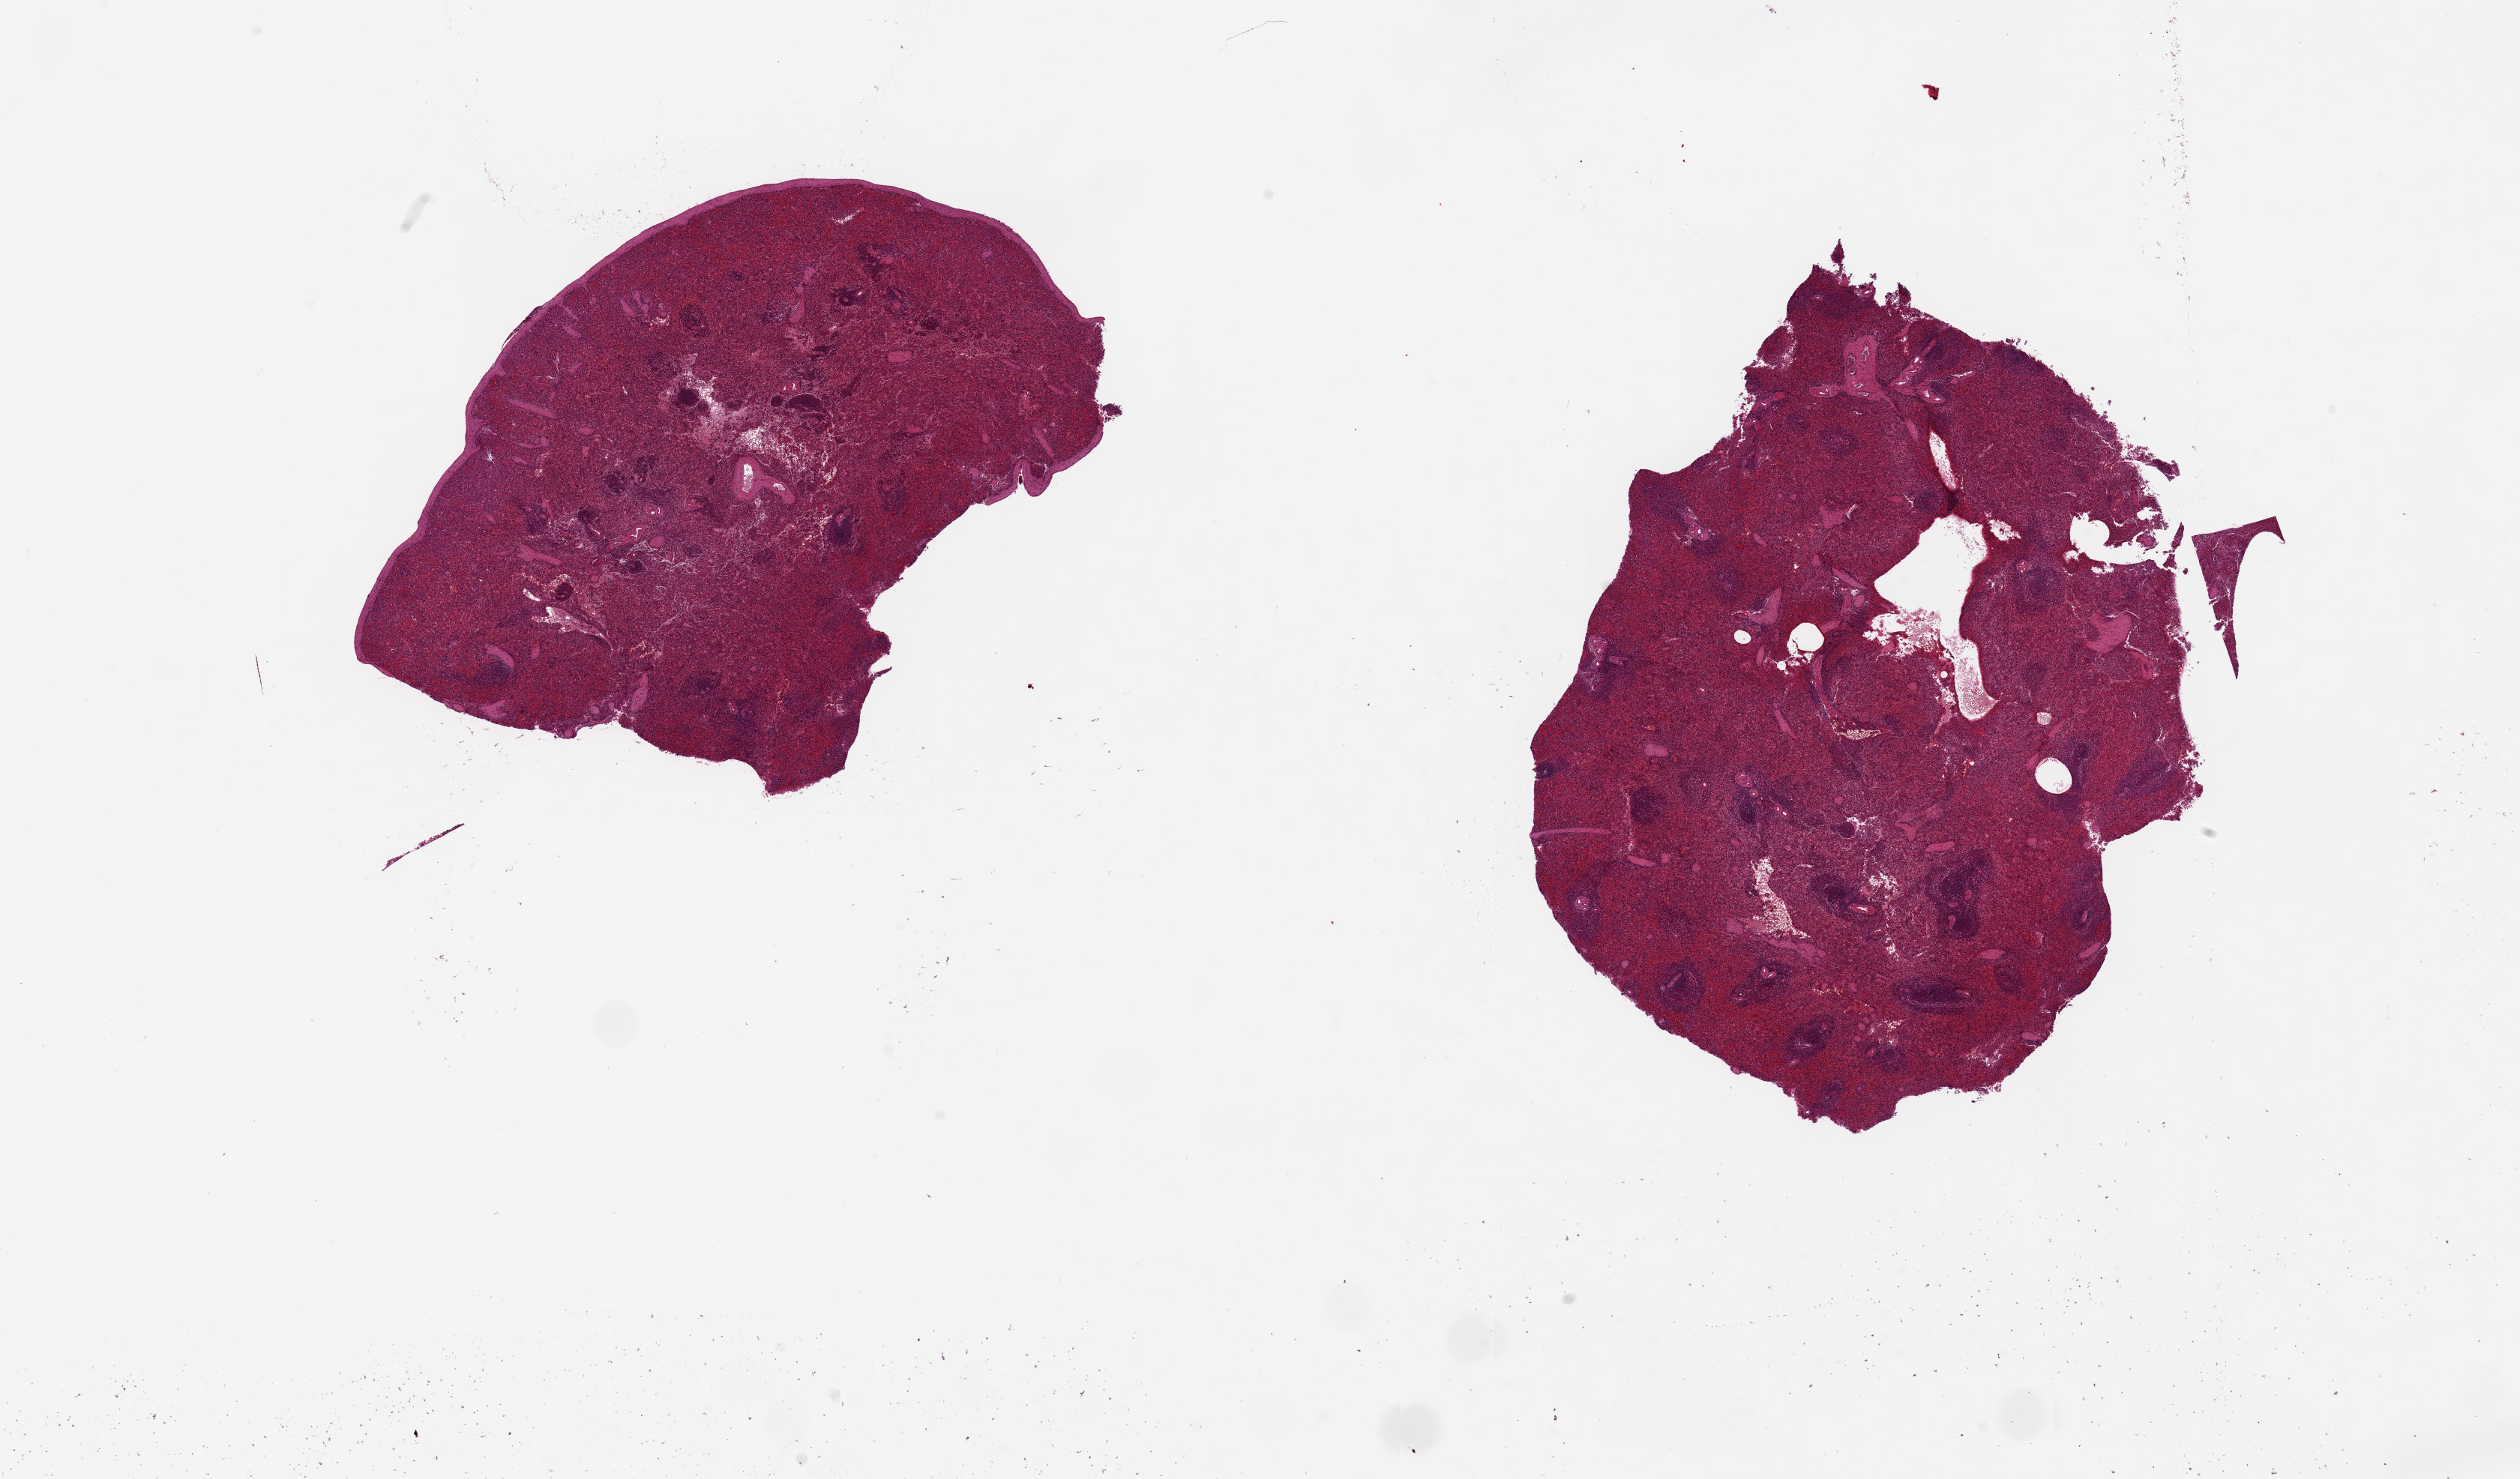
Digitized haematoxylin and eosin-stained section, a low-resolution overview of the entire scanned area, about 26.6 x 15.6 mm, PAXgene-fixed, paraffin-embedded tissue, sampled site (target tissue): spleen, tissue donor sample.
Review note (as recorded): 2 pieces, 8x7 & 7x6mm; hemorrhages & fractures (traumatic?); moderately congested.